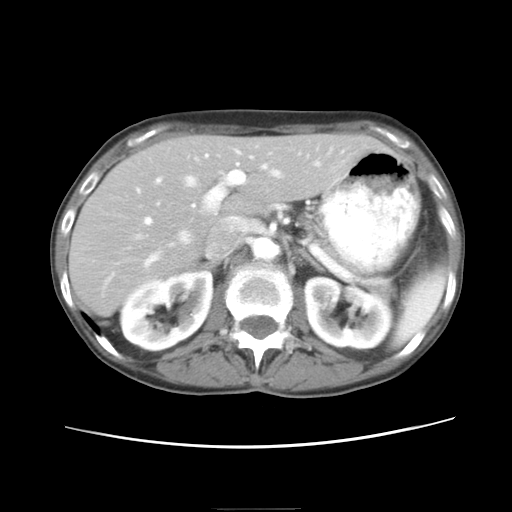
Contrast-enhanced abdominal CT, one axial slice; position 14 of 26 along the scan axis; 120 kVp; intravenous contrast given; soft-tissue window (W 400 / L 40 HU); 7.5 mm slice thickness; 512 × 512 image matrix. Female patient, age 65 years. From the clinical record (not read from this slice): diagnosis: colorectal cancer liver metastases, imaged before liver resection; multiple liver metastases: no; disease in both lobes: yes; chemotherapy before resection: yes.
Annotated regions visible in this slice (expert manual segmentation):
- hepatic veins: bounding box <144,152,319,265> (left, top, right, bottom; pixels)
- liver: <72,136,373,312>
- planned liver remnant (the part of the liver to remain after resection): <72,136,373,312>
- portal vein (with intrahepatic branches): <137,149,266,224>